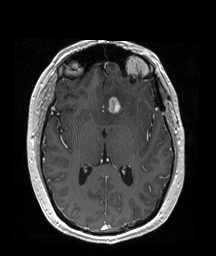
Brain MRI from a brain-tumour surgery series, one axial slice; T1-weighted post-contrast; 1 mm slice thickness; 216 × 256 image matrix, field of view 211 × 250 mm. Case-level facts recorded for this patient, not image findings: histopathology: Oligodendroglioma; WHO grade: 2; IDH mutation: yes.
Outlined on this slice (outlined manually by an expert reader):
- tumour: box from (x=115, y=96) to (x=128, y=112) px